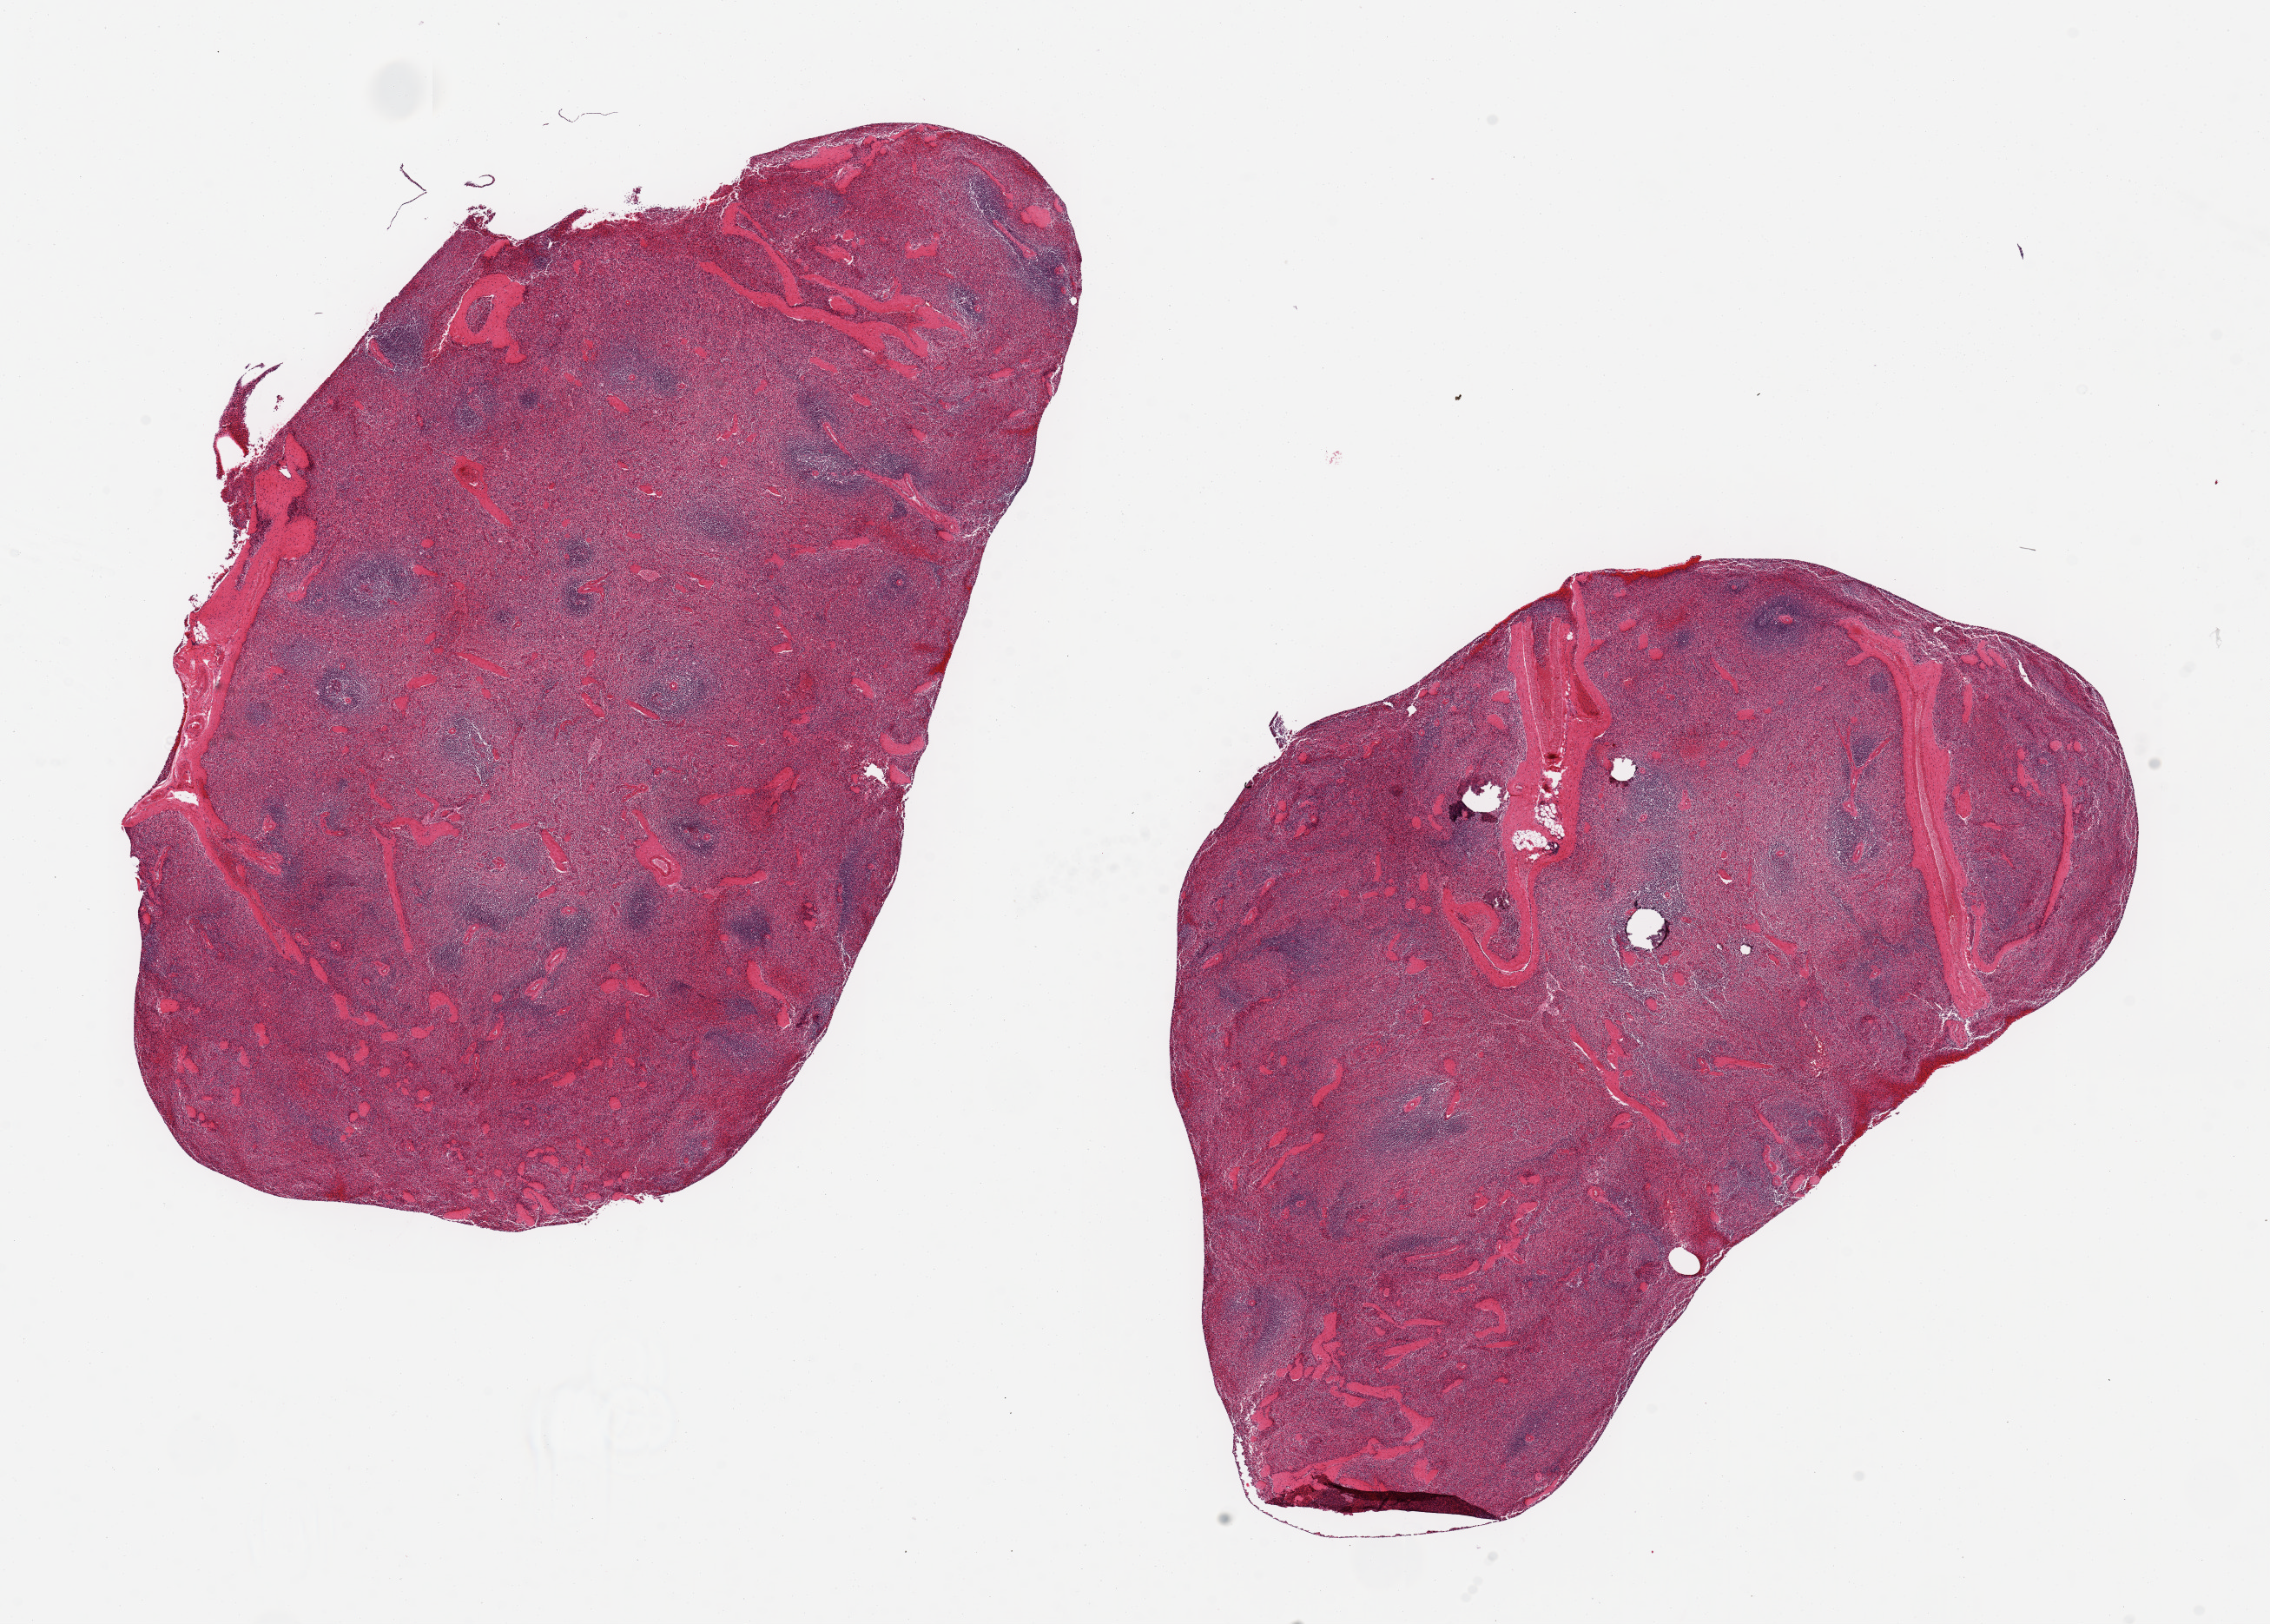
Digitized H&E-stained section, brightfield, shown as a low-resolution overview of the whole scanned area (about 20.7 x 14.8 mm); PAXgene-fixed paraffin-embedded (PFPE) section; target tissue: spleen; donor tissue sample. Male donor.
Review note (as recorded): 2 pieces ~11x6 mm.